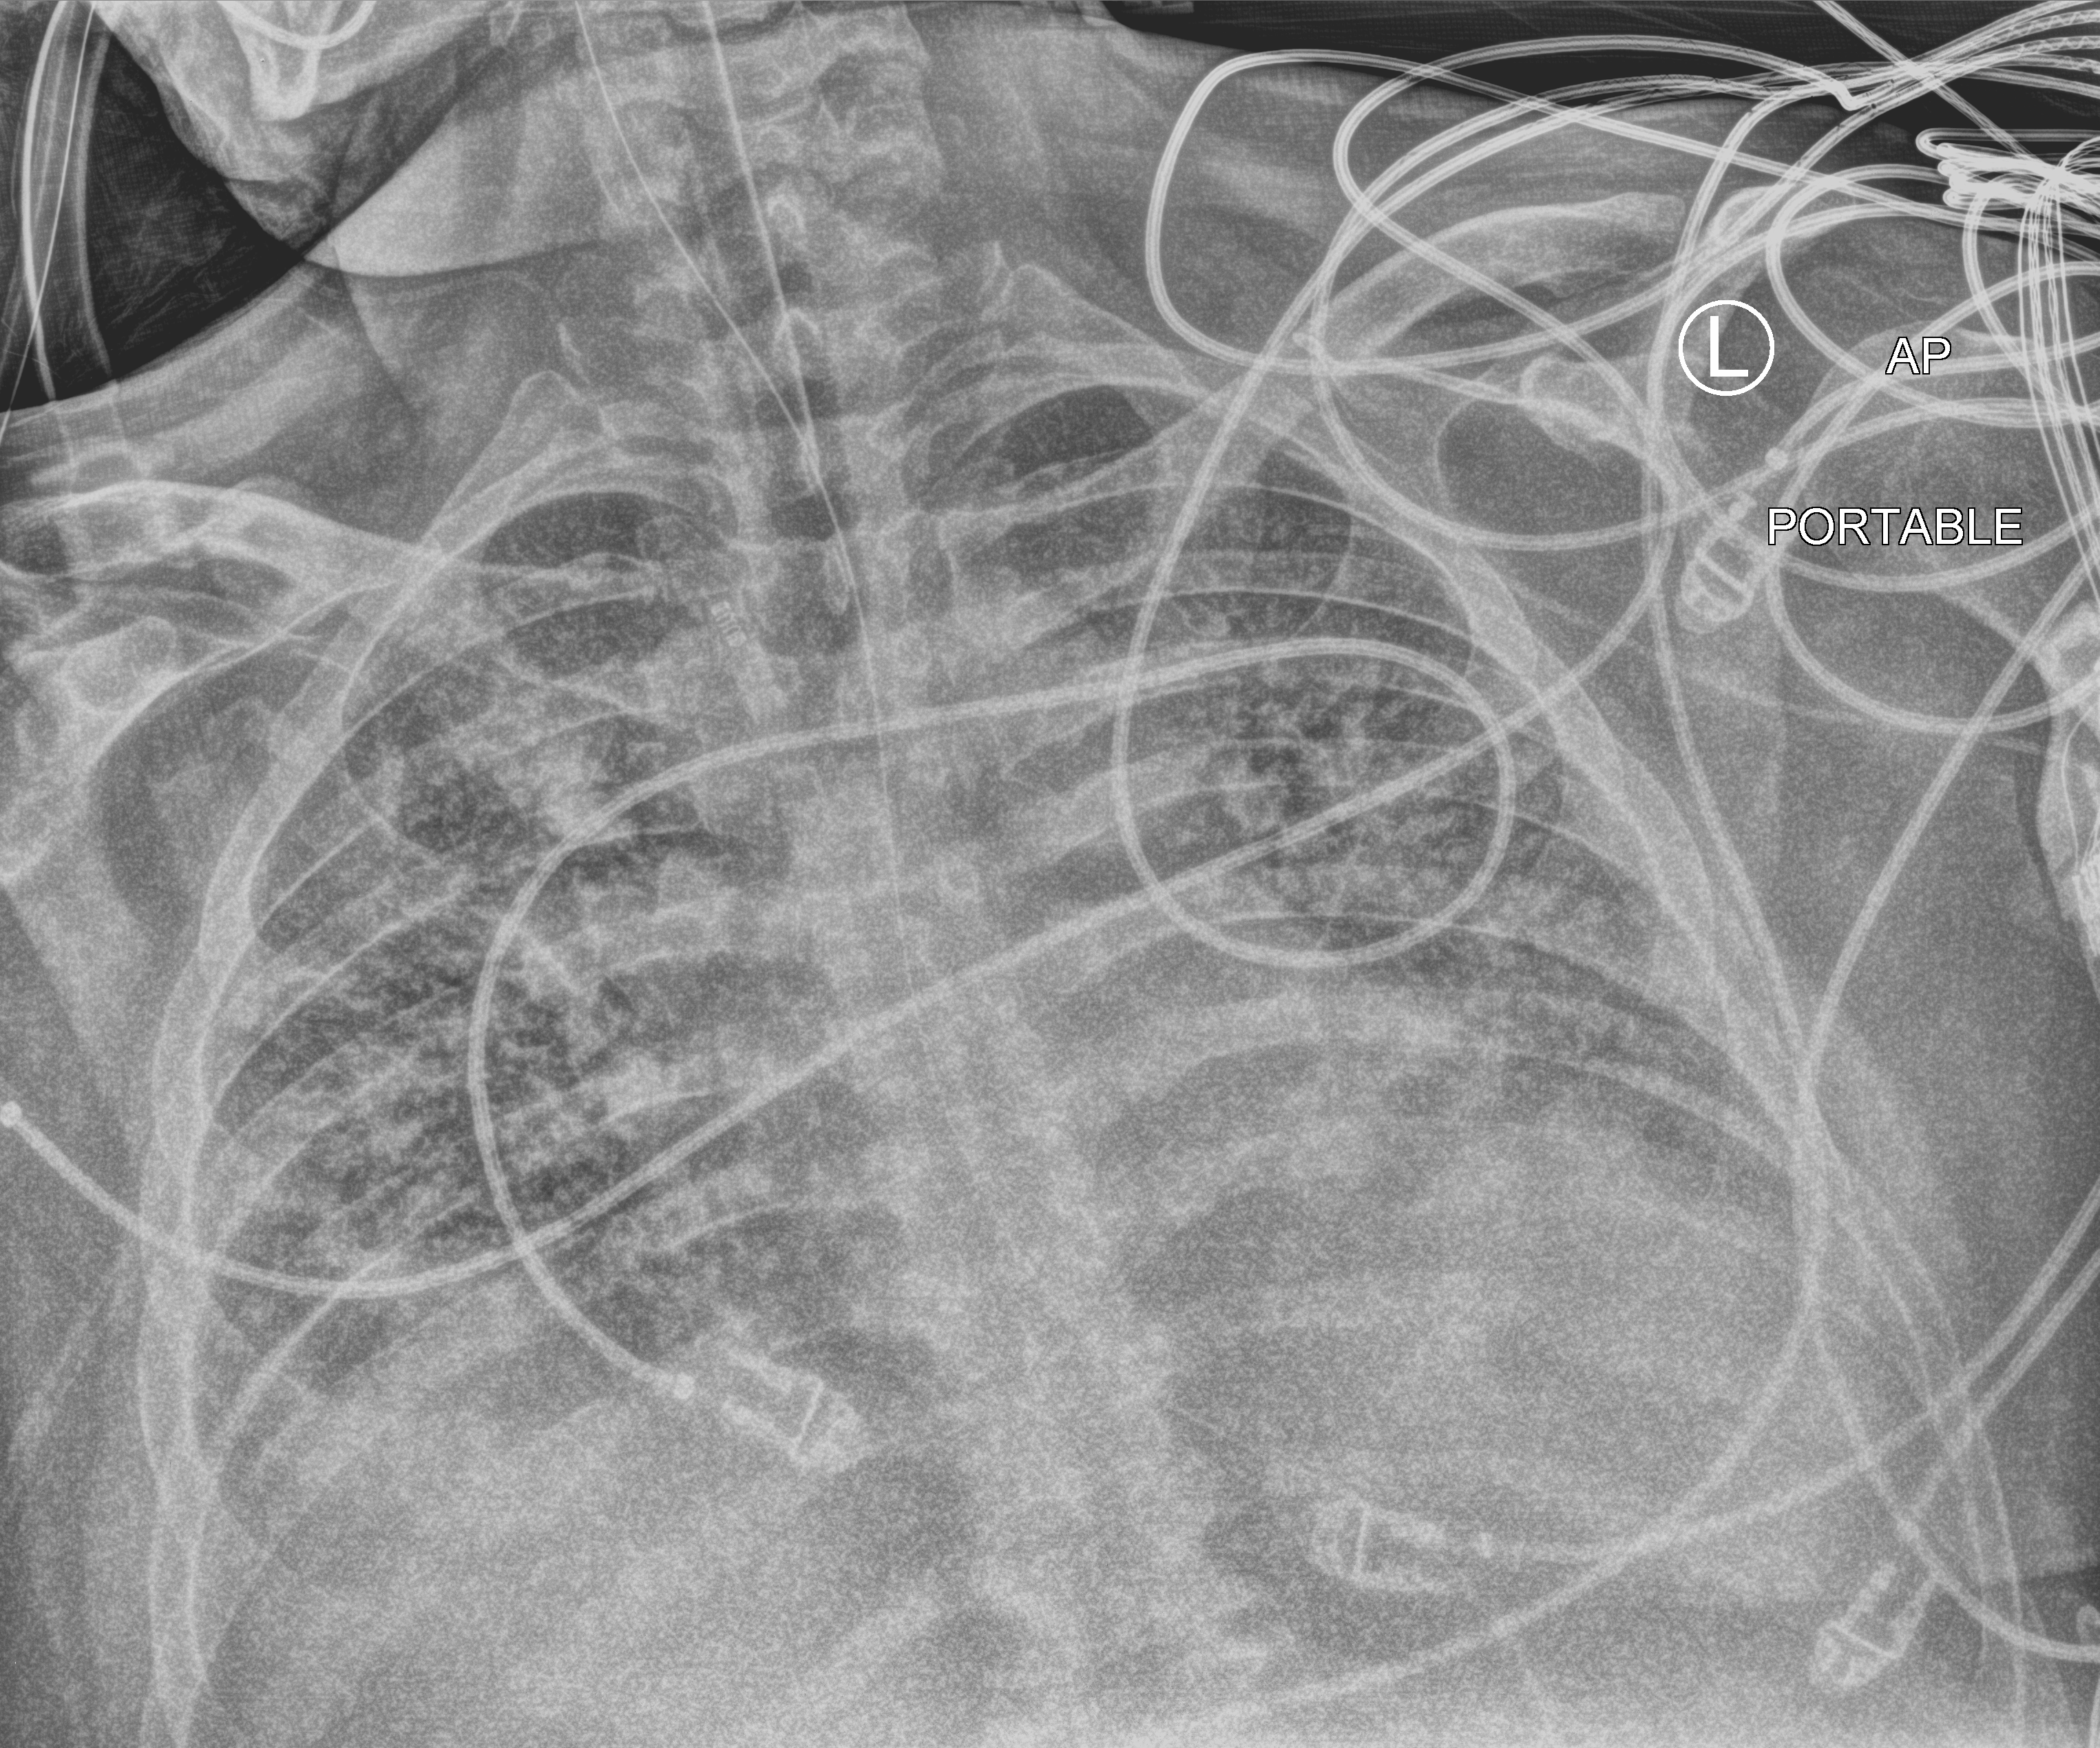
Portable chest radiograph, anteroposterior (AP) projection. Patient hospitalised with COVID-19, aged 18–59 years.
From the hospital-stay record, not from the radiograph (when in the stay this image was taken is not recorded): mechanically ventilated during this hospital stay: yes.